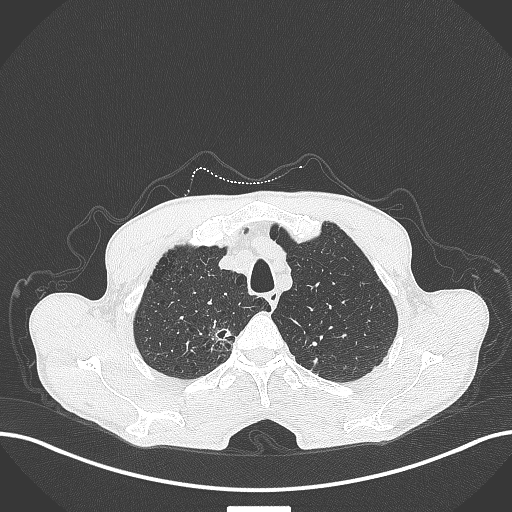
Chest CT, one axial slice. Position 363 of 445 along the scan axis. Reconstruction kernel B70f. 120 kVp. Lung window (W 1500 / L -600 HU). 512 × 512 image matrix, field of view 400 × 400 mm. Patient: male, 70 years. From the clinical record (not read from this slice): clinical TNM (as recorded): T1a N0 M0; histopathological grade: G1-2.
Outlined on this slice (rectangle marked by the reading radiologist):
- lung tumour (recorded histology: adenocarcinoma): bounding box <208,319,234,344> (left, top, right, bottom; pixels)